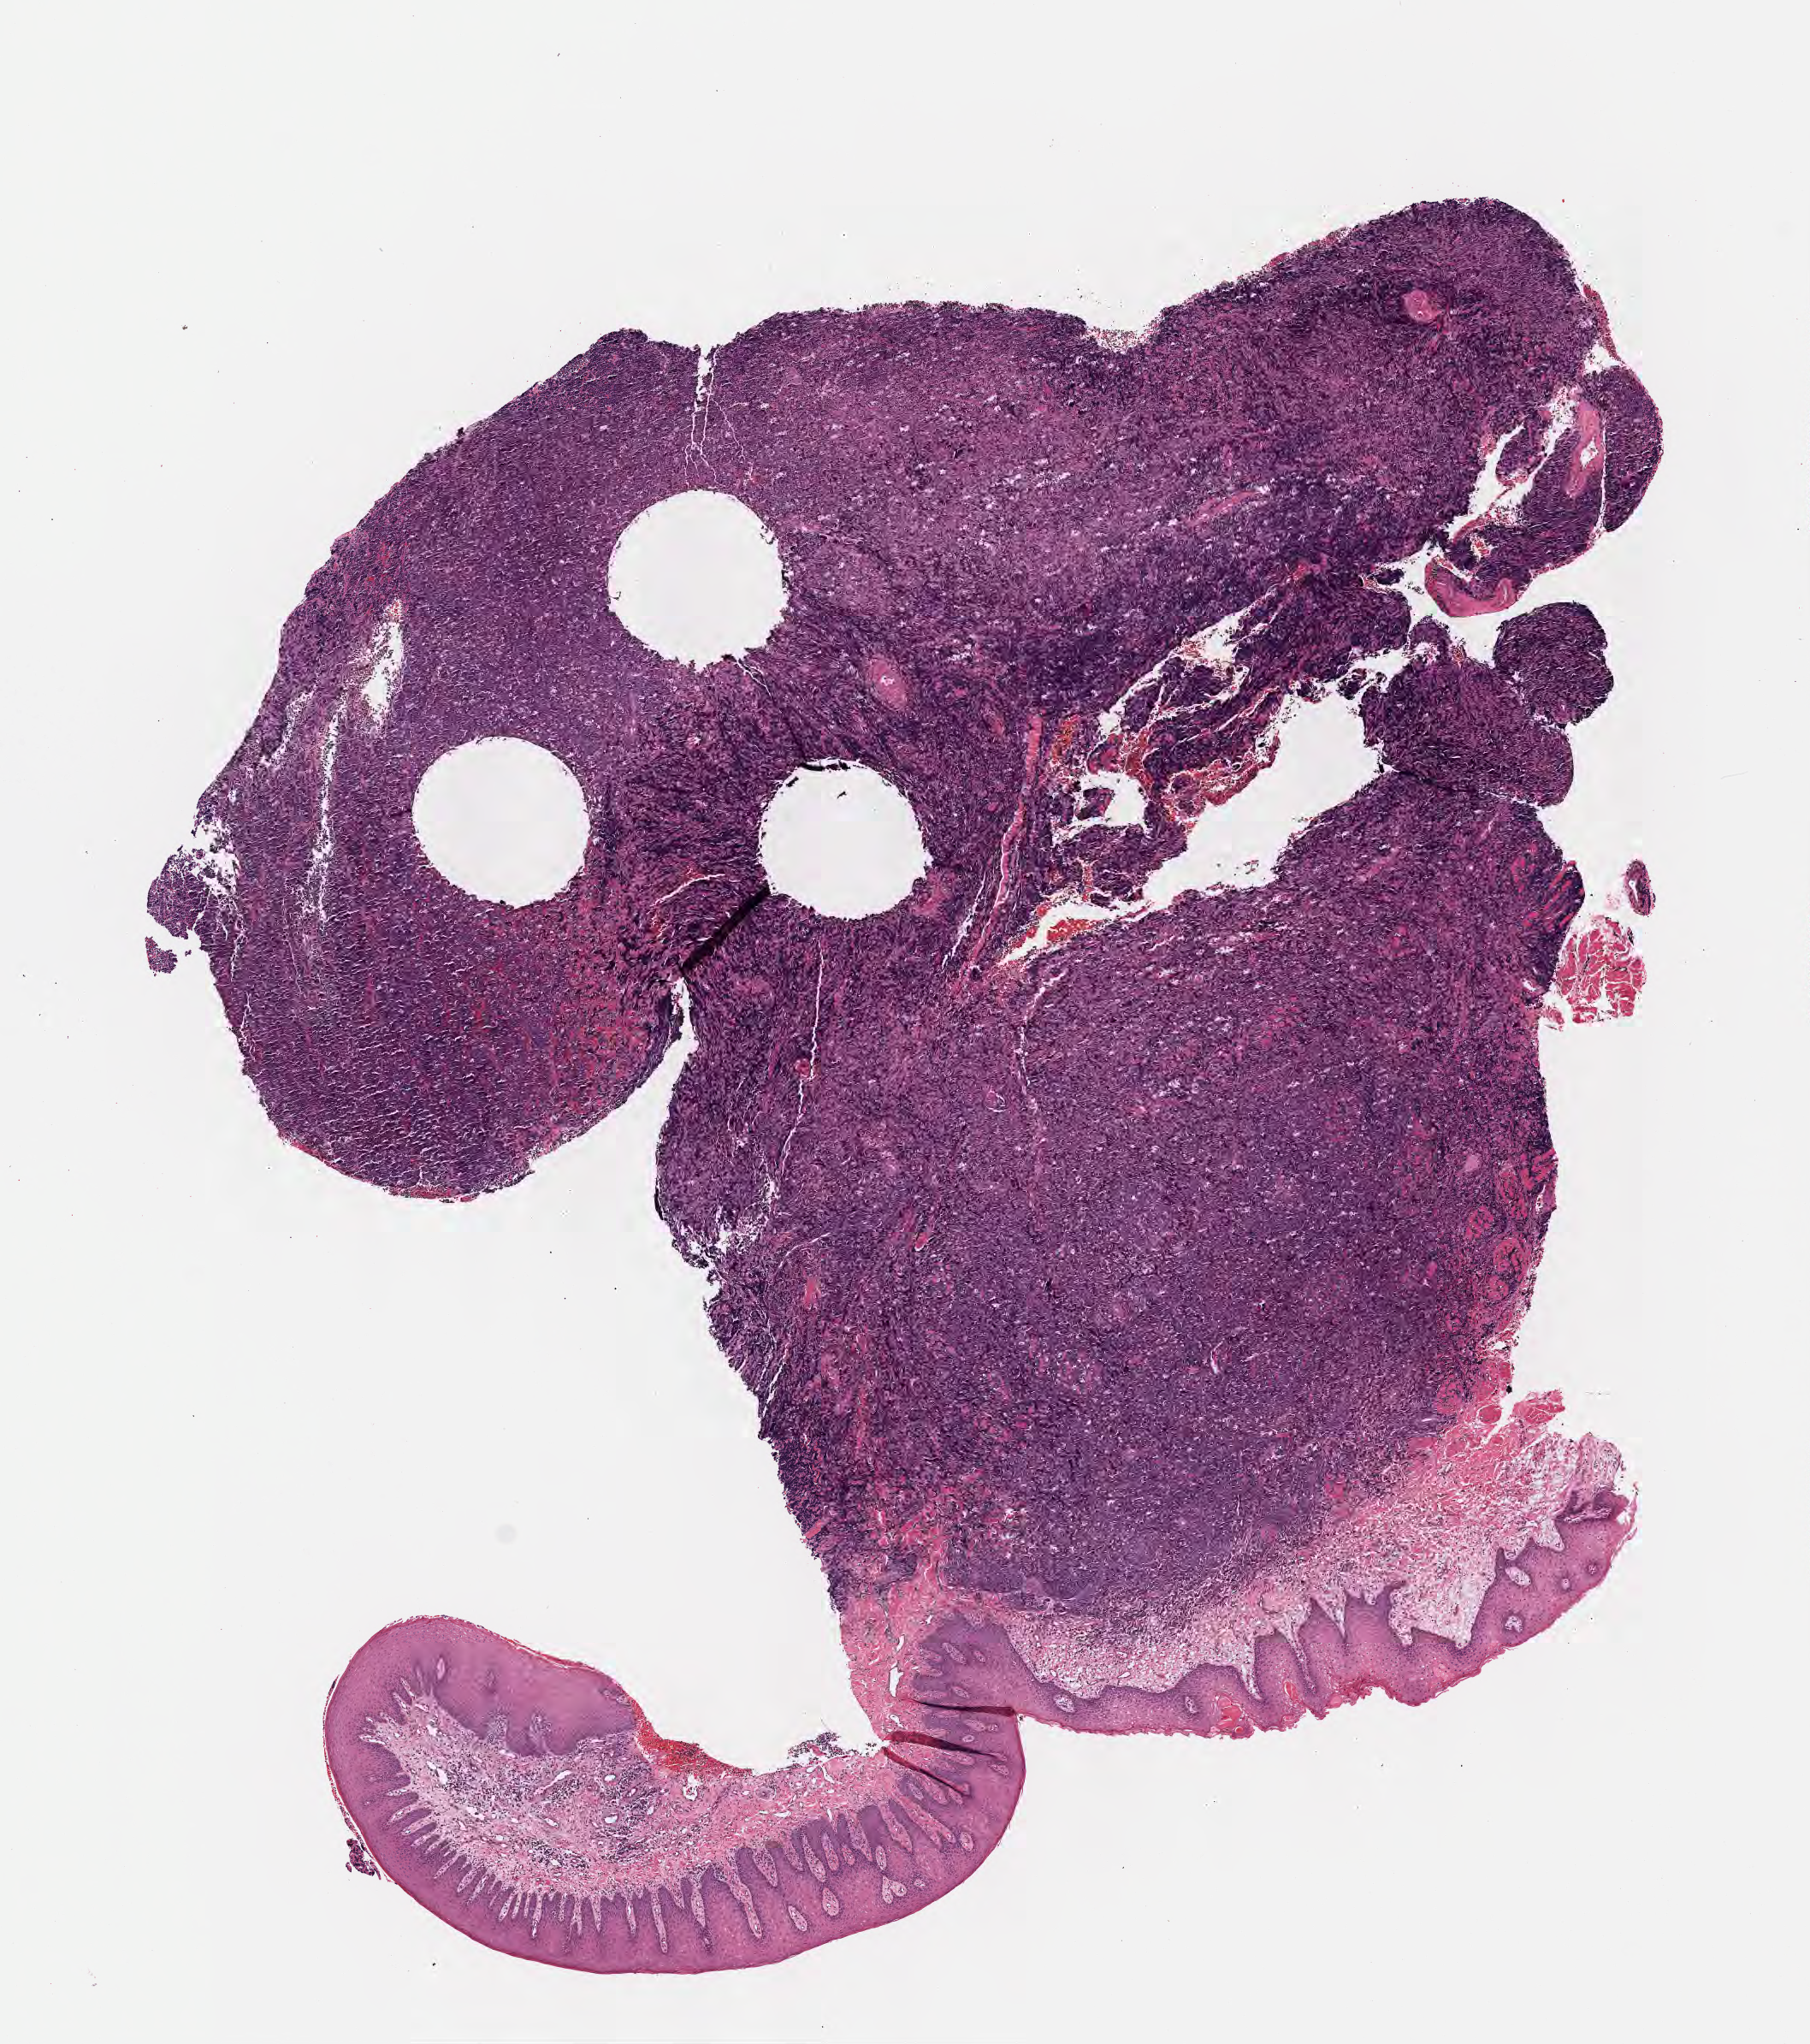
Digitized haematoxylin and eosin-stained section, low-resolution overview of the scanned area, about 8.6 x 9.7 mm. FFPE section. Specimen: primary tumor. Site: cranium. Patient: female, age at initial diagnosis 6 years. Composition of this section per pathologist review: tumor cells 80%, tumor nuclei 90%, stromal cells 10%, necrosis 0%, normal cells 10%. Infiltration values recorded for this section: lymphocyte infiltration 40%, monocyte infiltration 30%, neutrophil infiltration 5%.
Section: bottom of the tissue portion. Histologic diagnosis: Burkitt lymphoma, NOS. Ann Arbor stage (patient): Stage III.